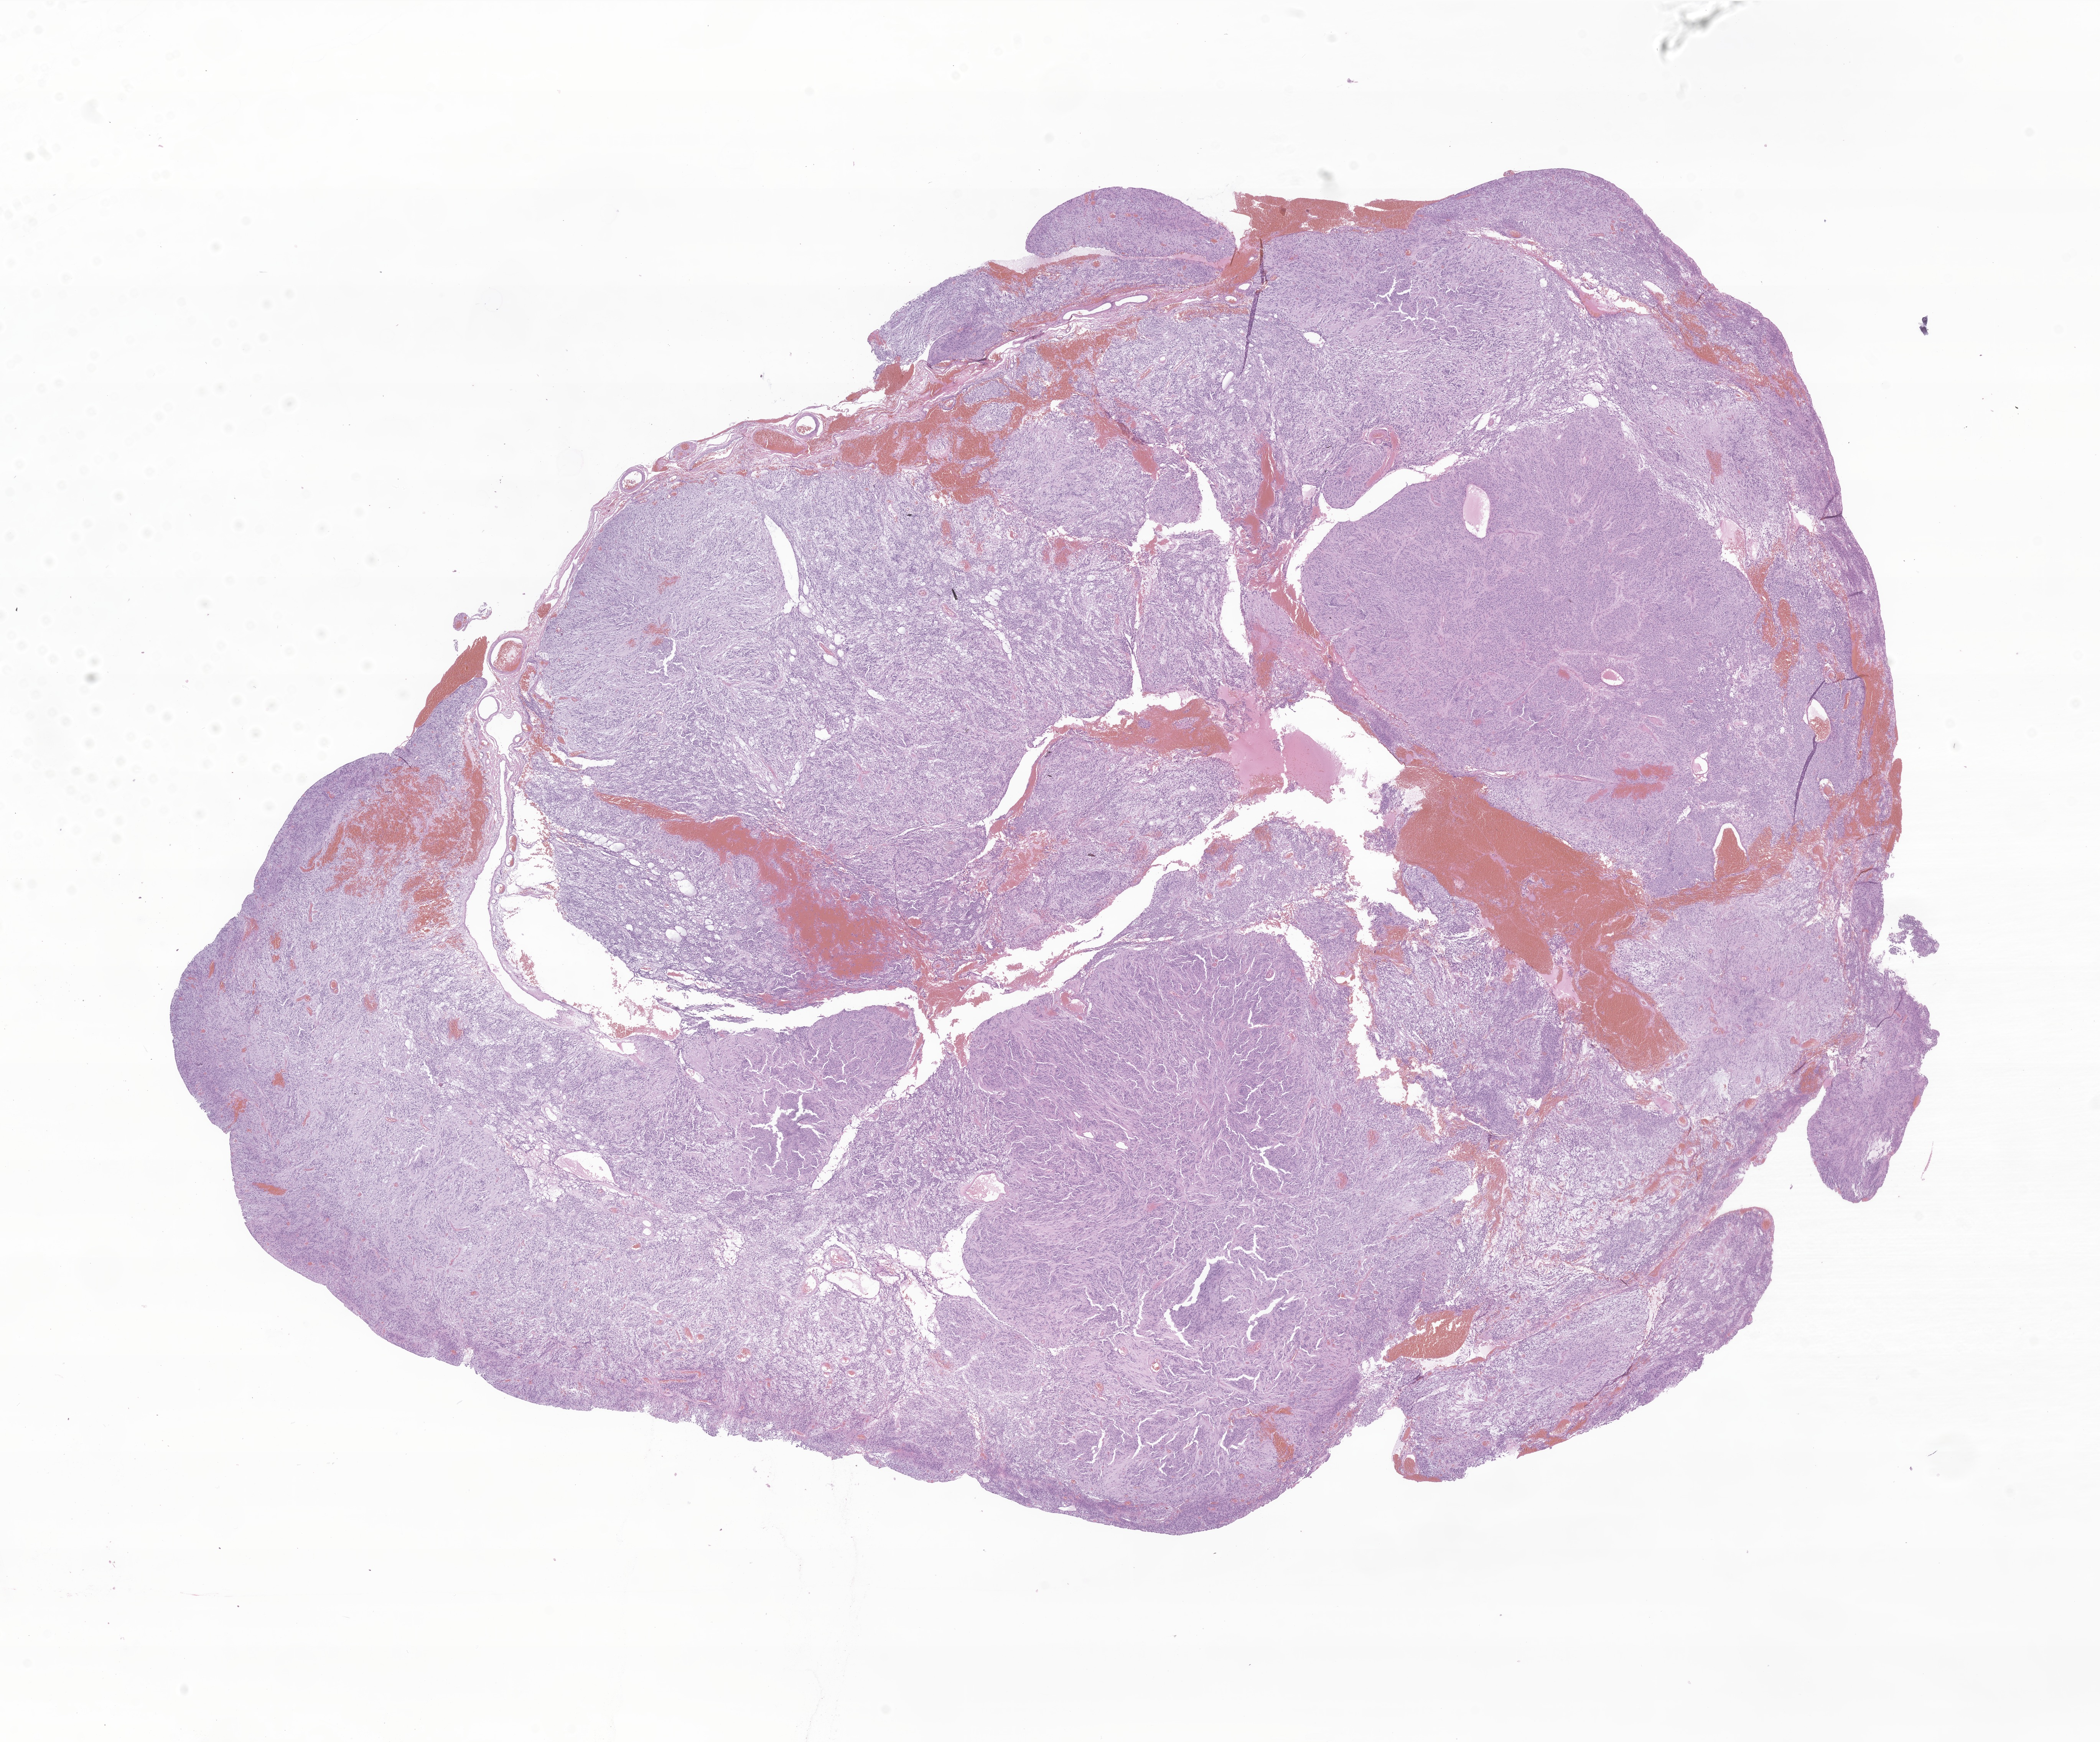
Hematoxylin and eosin (H&E) whole-slide image of tumor tissue from the spinal cord — whole scanned area (about 23.1 x 19.1 mm) shown as a low-resolution overview. Formalin-fixed, paraffin-embedded (FFPE) tissue. Patient: male, age 129 months (10 years 9 months).
Diagnosis (ICD-O-3 morphology term): Myxopapillary ependymoma.